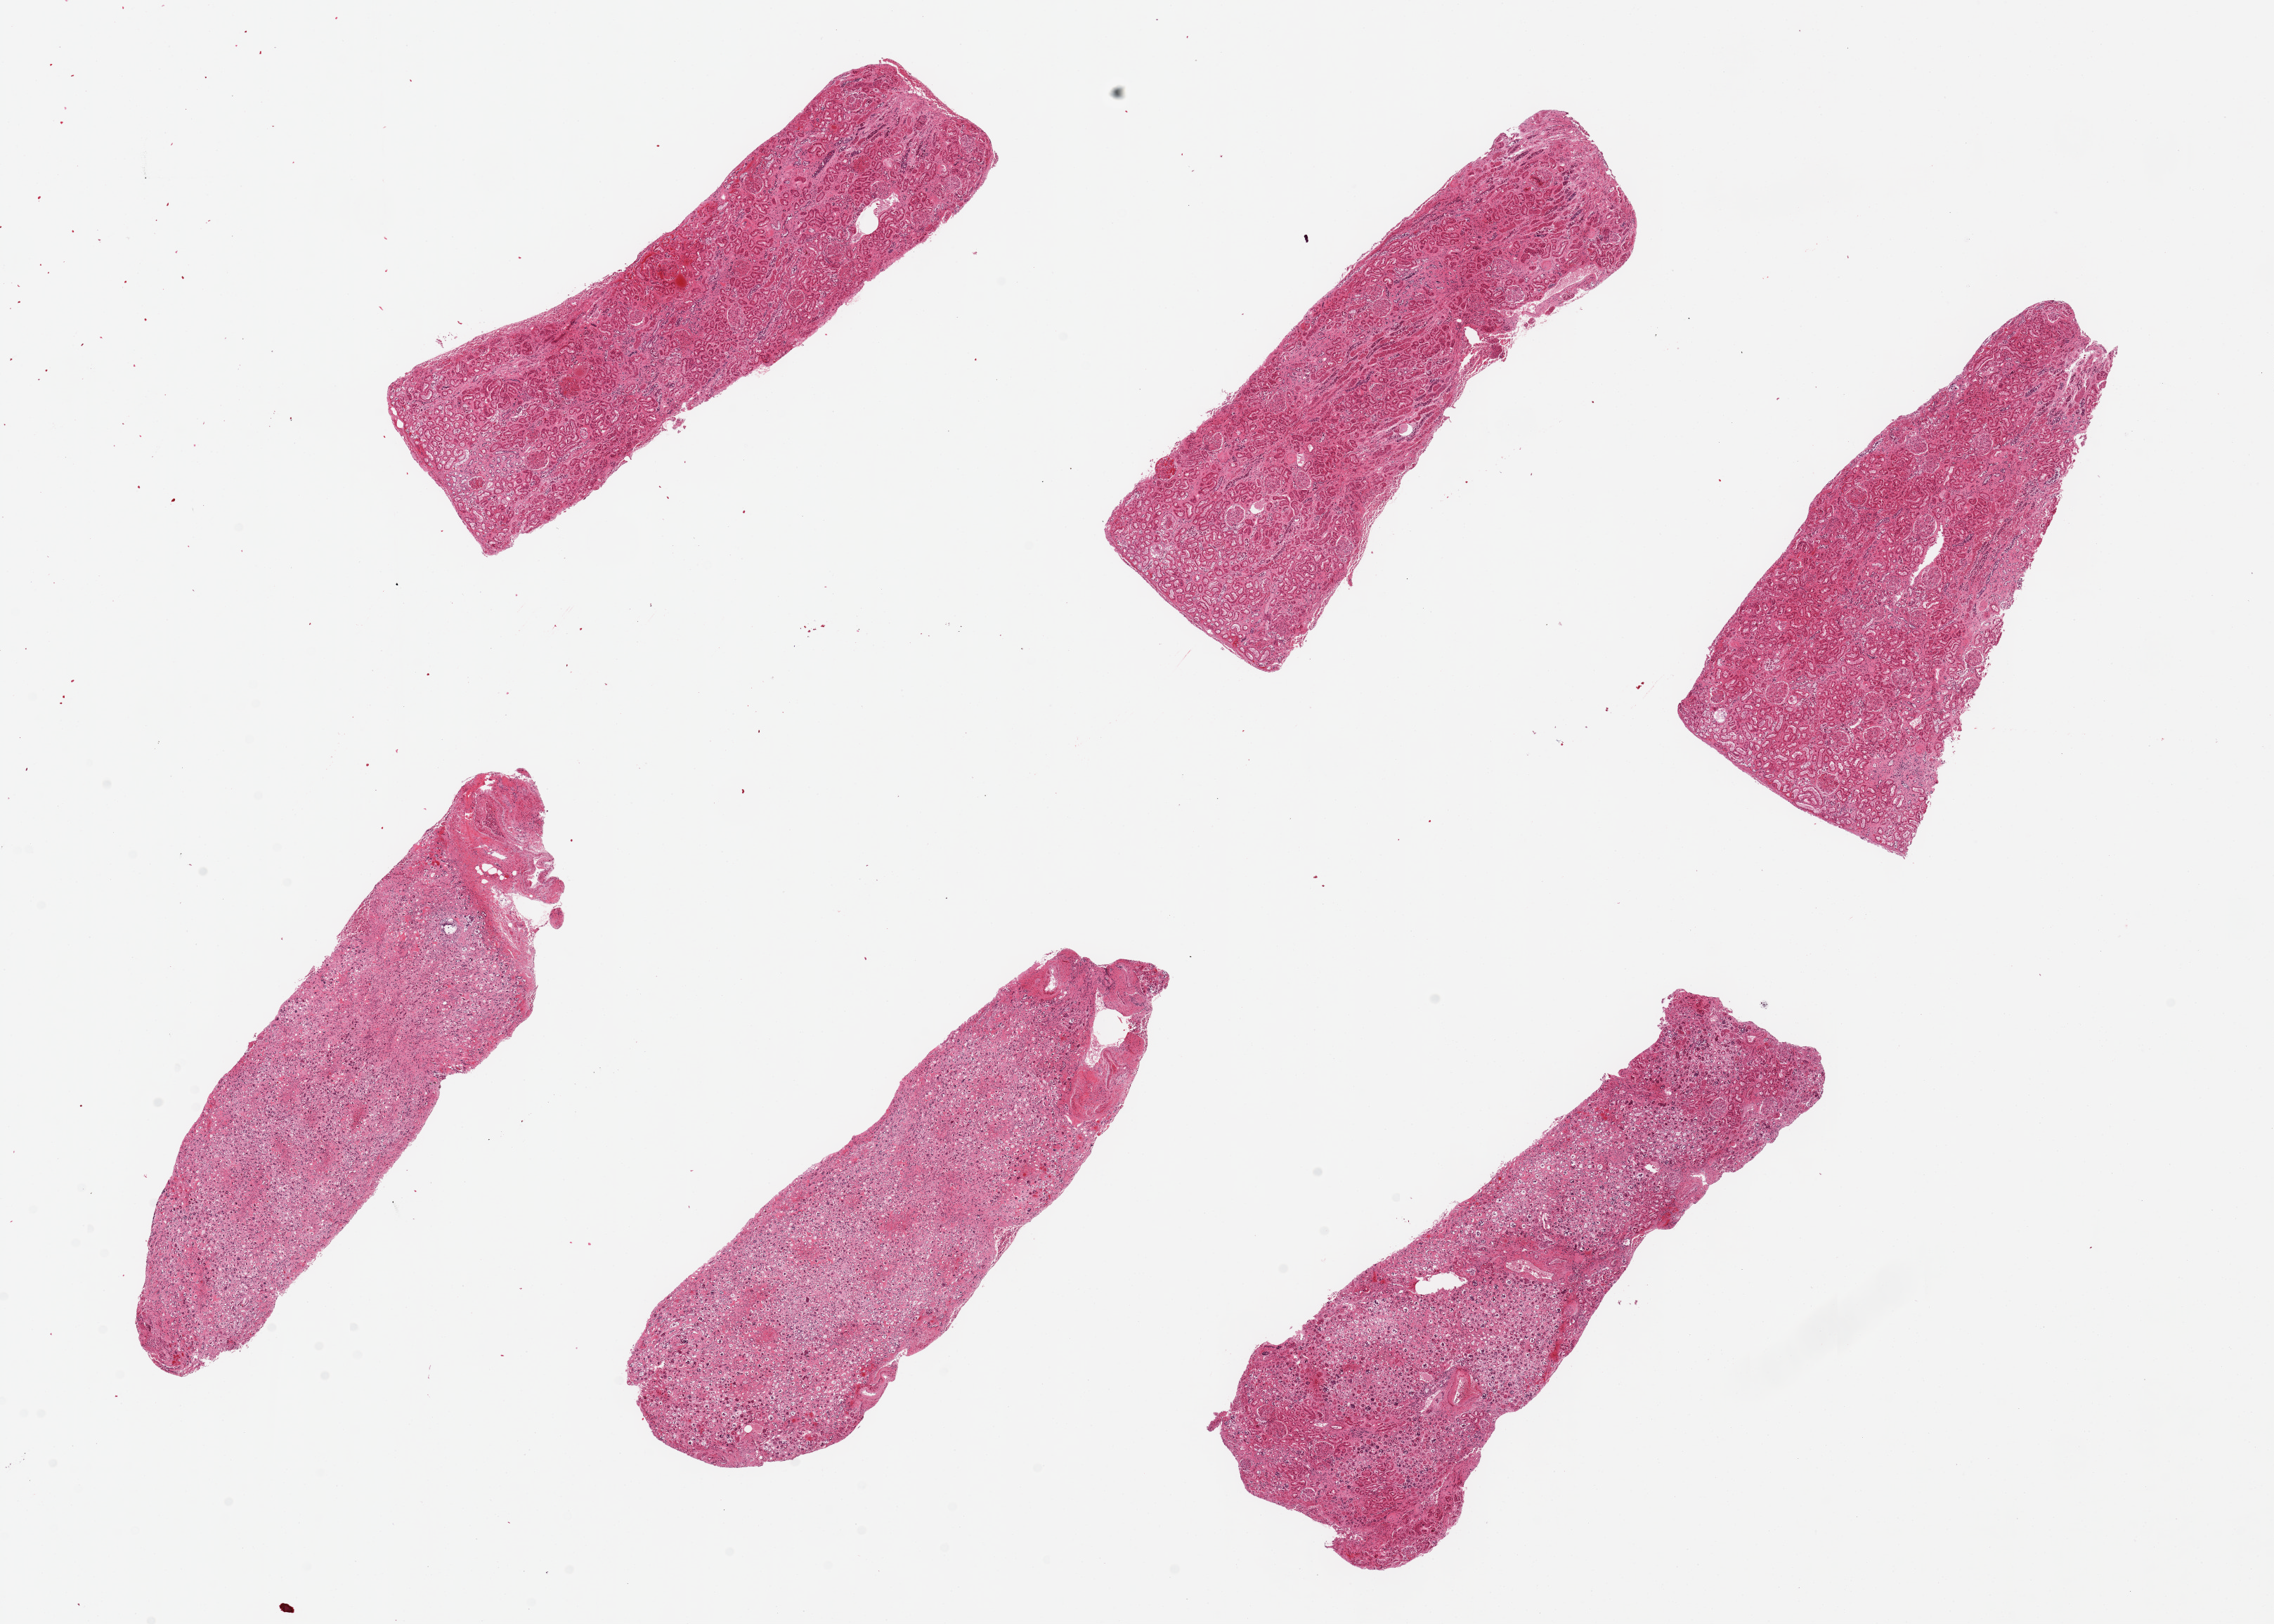
Hematoxylin and eosin (H&E) whole-slide image — low-resolution overview of the scanned area, about 25.6 x 18.3 mm (acquisition: 20x scan); PAXgene-fixed, paraffin-embedded tissue; sampled site (target tissue): renal cortex; tissue donor sample. Male donor.
Review note (as recorded): 6 pieces, up to 8x3mm.